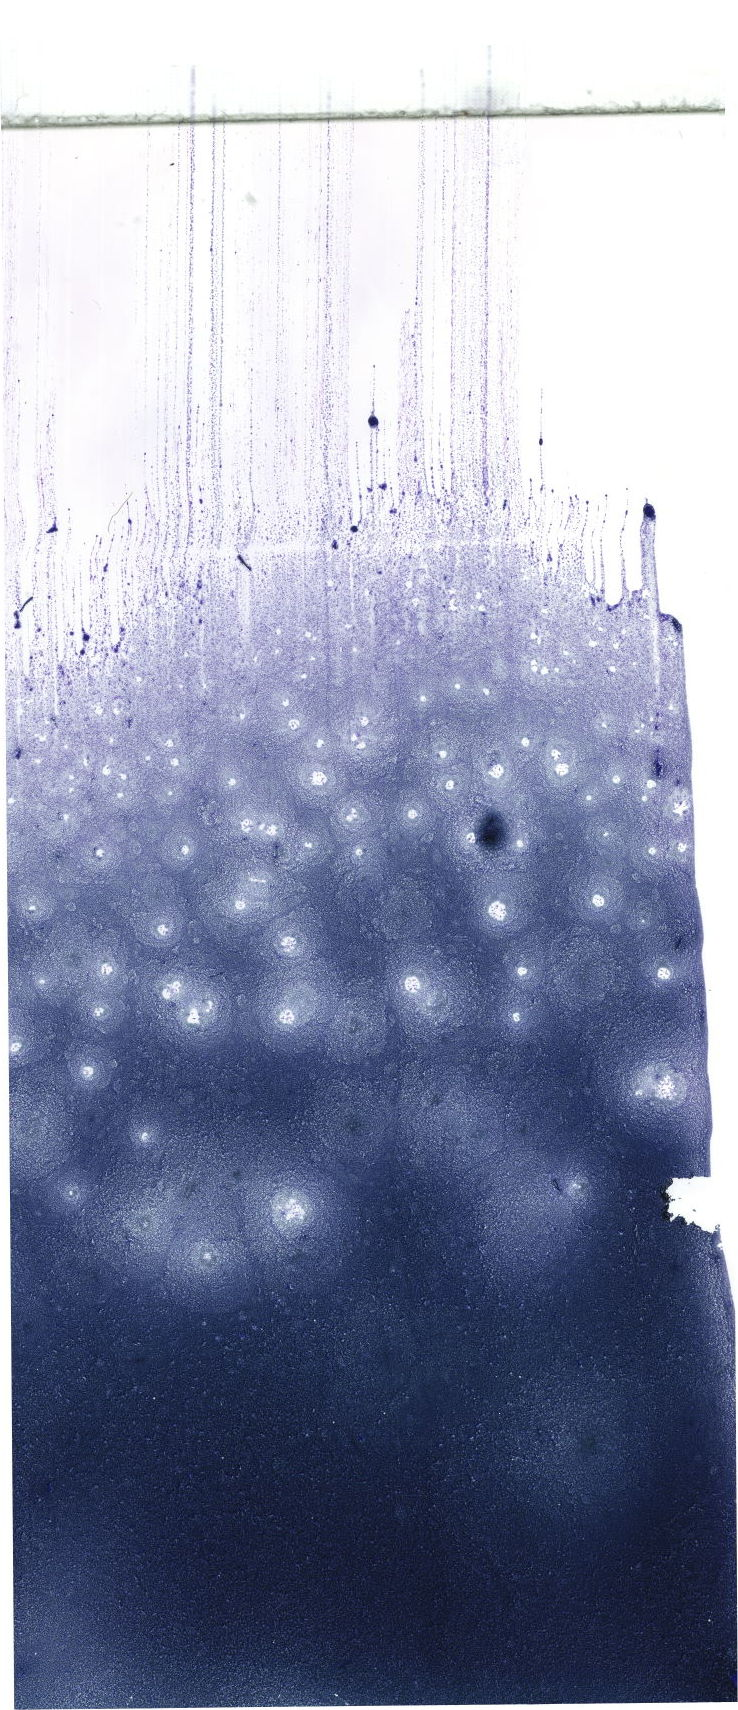
May-Grünwald–Giemsa-stained marrow aspirate smear (whole slide), shown as a low-resolution overview of the whole scanned area (about 20.9 x 48.5 mm). Patient sex: male.
Diagnosis: Chronic Phase Chronic Myeloid Leukemia, BCR-ABL1 Positive.